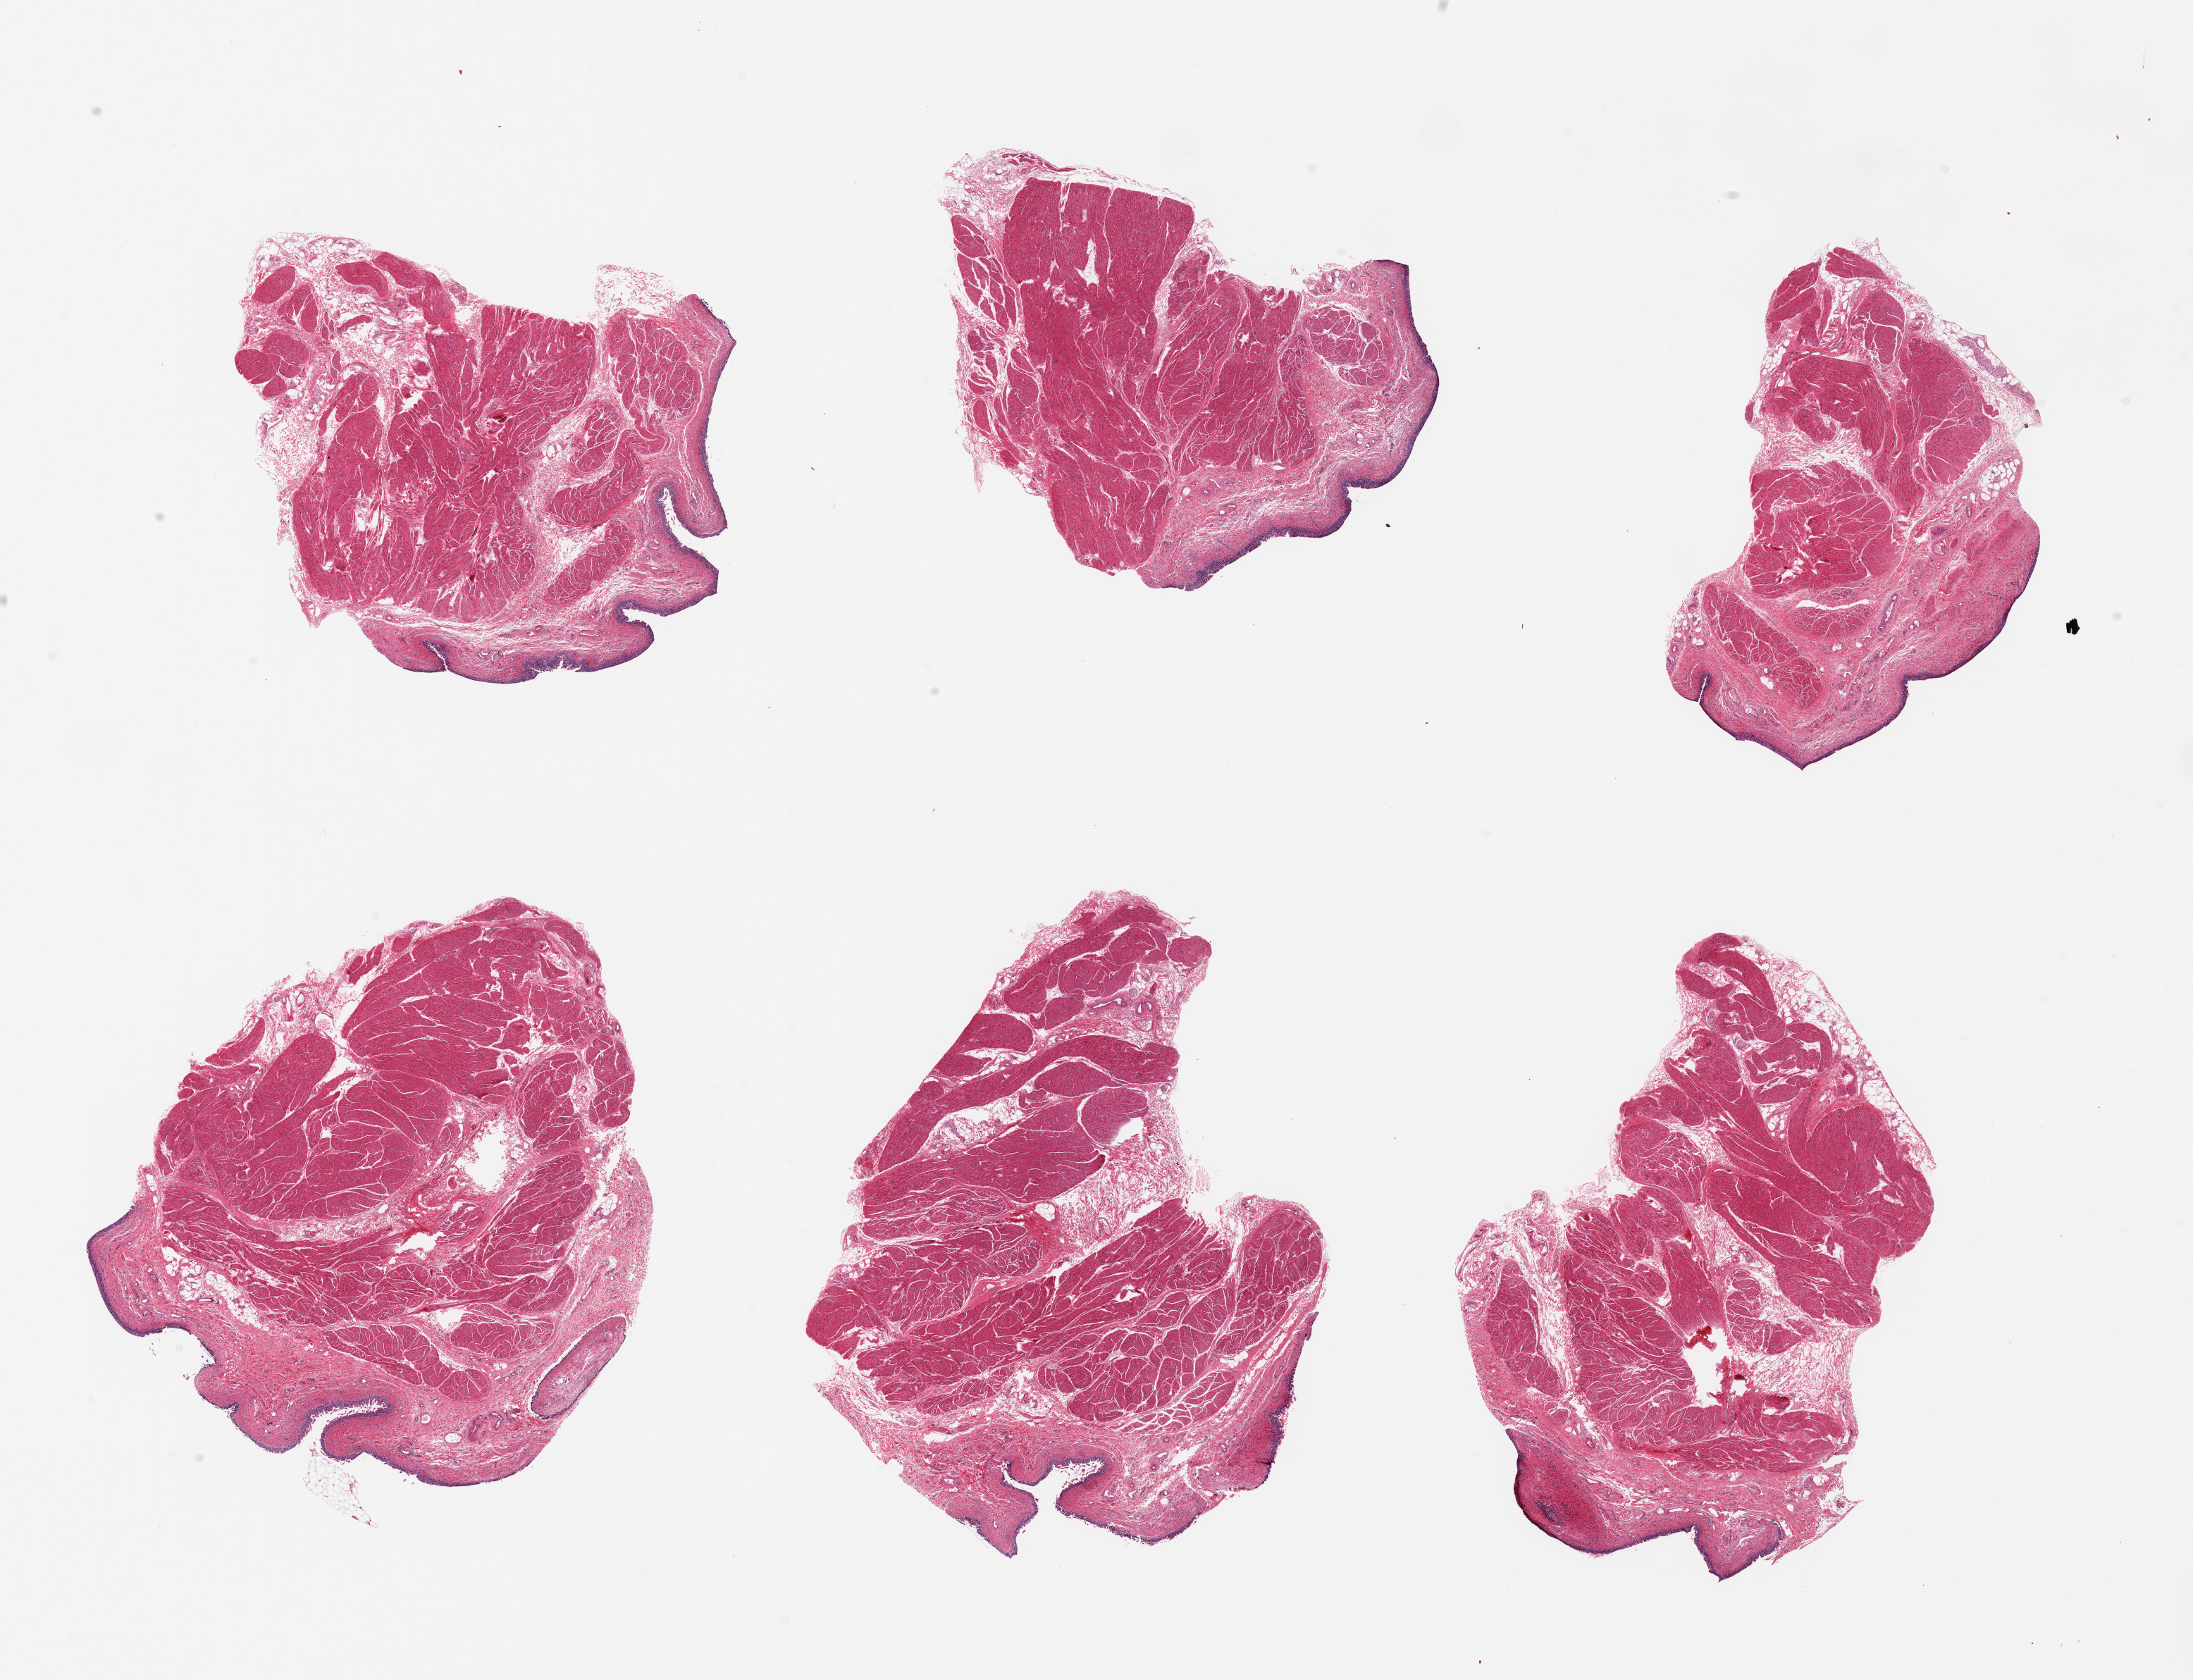
Whole-slide image, H&E stain, brightfield — a low-resolution overview of the entire scanned area, about 24.6 x 18.9 mm (acquisition: 20x scan), PAXgene-fixed paraffin-embedded (PFPE) section, section of urinary bladder (target tissue), donor tissue sample. Donor sex: female.
Pathologist's review note for this sample: 6 pieces up to 7x5 mm; partly sloughed mucosa.